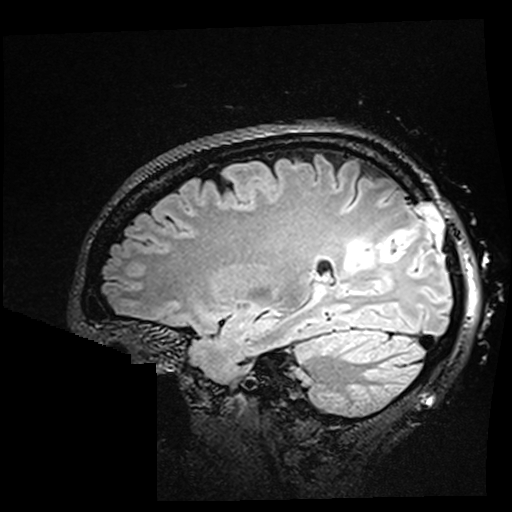
Brain MRI from a brain-tumour surgery series, one sagittal slice. Position 117 of 176 along the scan axis. T2 FLAIR. 512 × 512 image matrix, field of view 250 × 250 mm. From the clinical record (not read from this slice): histopathology: Oligodendroglioma; WHO grade: 2; IDH mutation: yes; tumour location: Right Parietal.
Outlined on this slice (manually delineated by an expert):
- residual tumour: bounding box (x1, y1, x2, y2) in pixels: (344, 238, 389, 280)